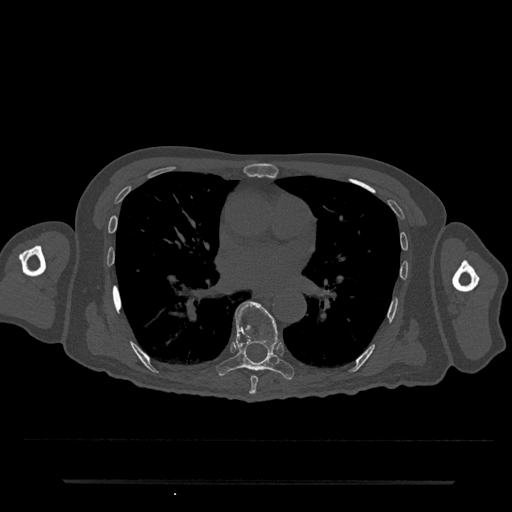
CT including the spine, one axial slice. Slice 436 of 797 in the series (ordered by position). 120 kVp. Bone window (W 1800 / L 400 HU). 512 × 512 image matrix, field of view 427 × 427 mm. Patient: male, 74 years. Case-level facts recorded for this patient, not image findings: primary cancer: prostate.
Structures marked on this image (semi-automatic segmentation, software-assisted and operator-edited):
- T7 vertebra: bounding box <249,376,258,395> (left, top, right, bottom; pixels)
- T8 vertebra: <216,301,294,381>